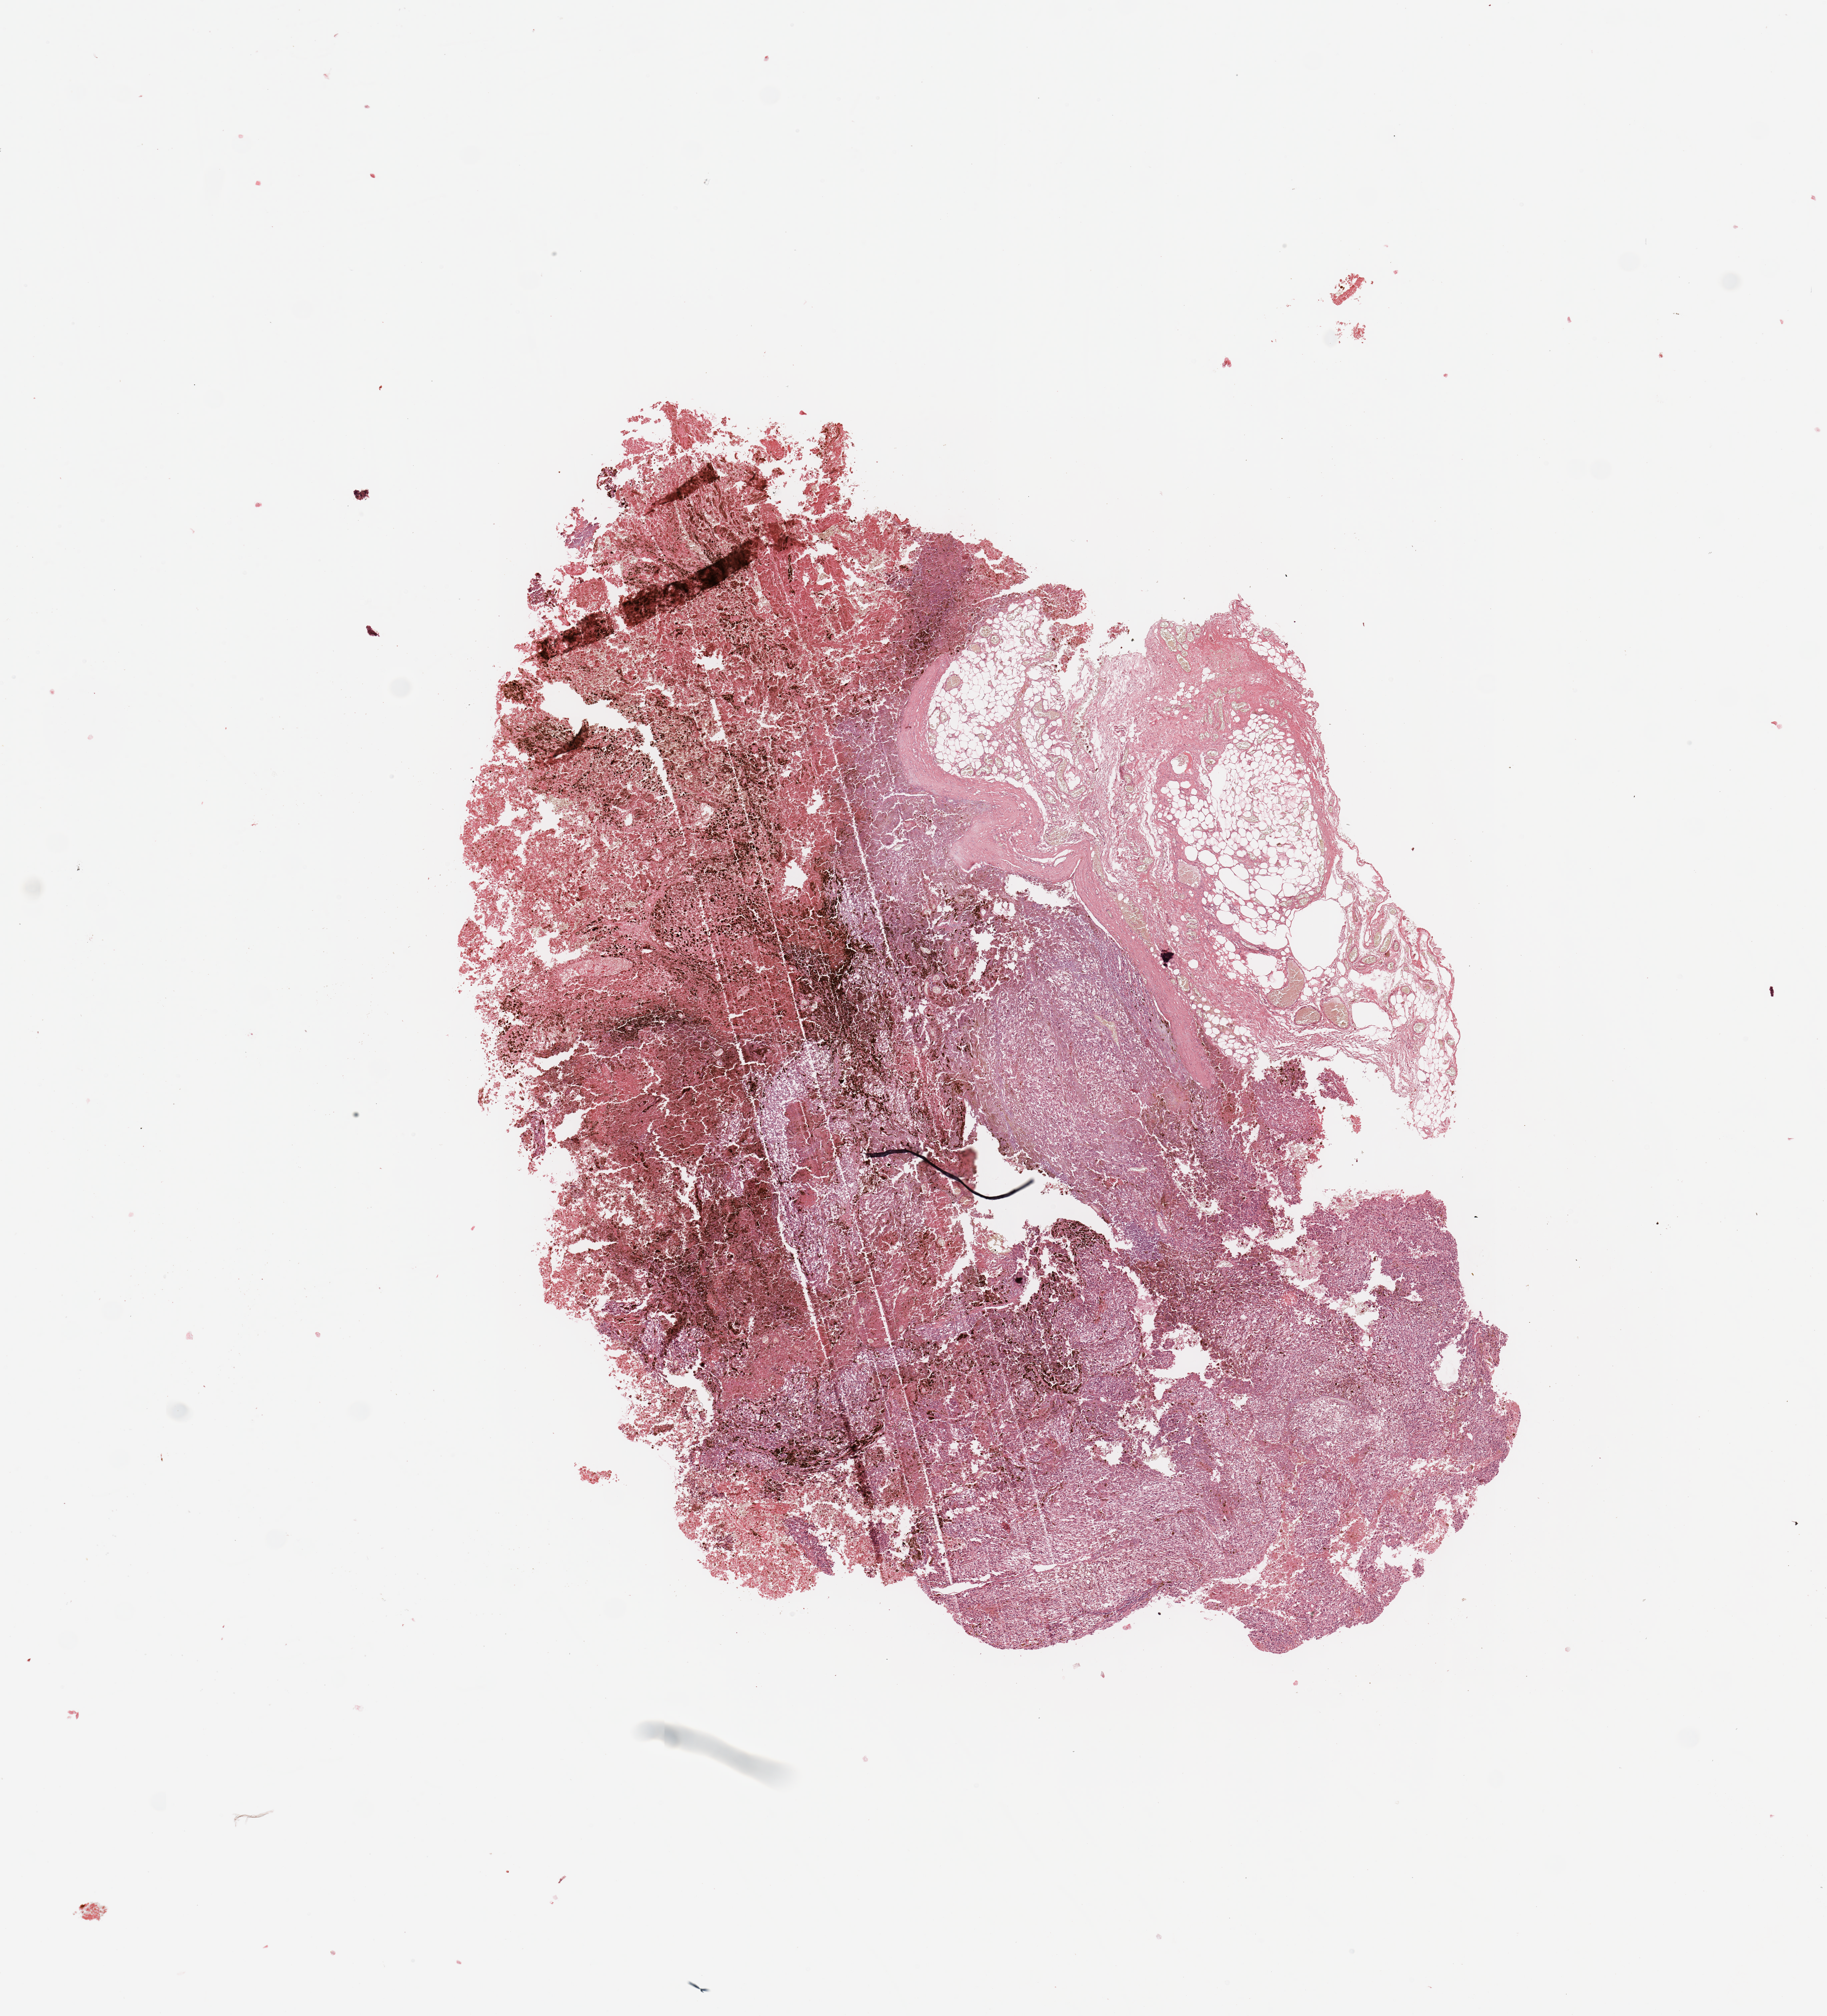
H&E whole-slide image — shown as a low-resolution overview of the whole scanned area (about 10.8 x 11.9 mm, acquisition: 20x scan), melanoma tumour tissue; sampled site not recorded. 63-year-old female patient.
Diagnosis: Malignant melanoma, NOS. Primary tumour site (as recorded): extremities. AJCC pathologic stage: IIC.